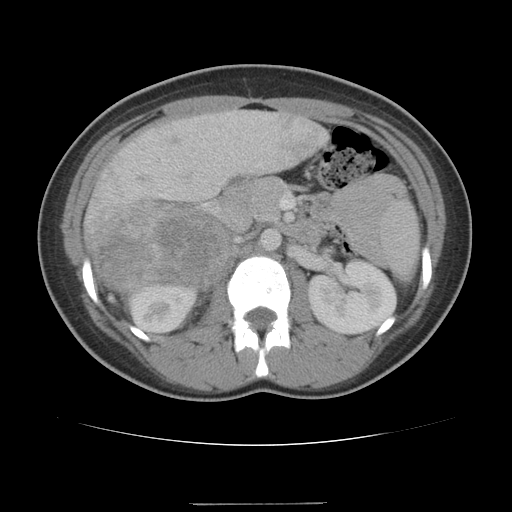
Contrast-enhanced abdominal CT, one axial slice. Position 64 of 100 along the scan axis. Reconstruction kernel STANDARD. 120 kVp. Intravenous contrast given. Soft-tissue window (W 400 / L 40 HU). 5 mm slice thickness. 512 × 512 image matrix, field of view 360 × 360 mm. Female patient, age 21 years. From the clinical record (not read from this slice): diagnosis: adrenocortical carcinoma; tumour side: right adrenal; tumour size at pathology: 15.5 cm; Ki-67 index: 26 %; stage (as recorded): 3.
Outlined on this slice (semi-automatically segmented with operator editing):
- mass: bounding box <101,203,227,293> (left, top, right, bottom; pixels)